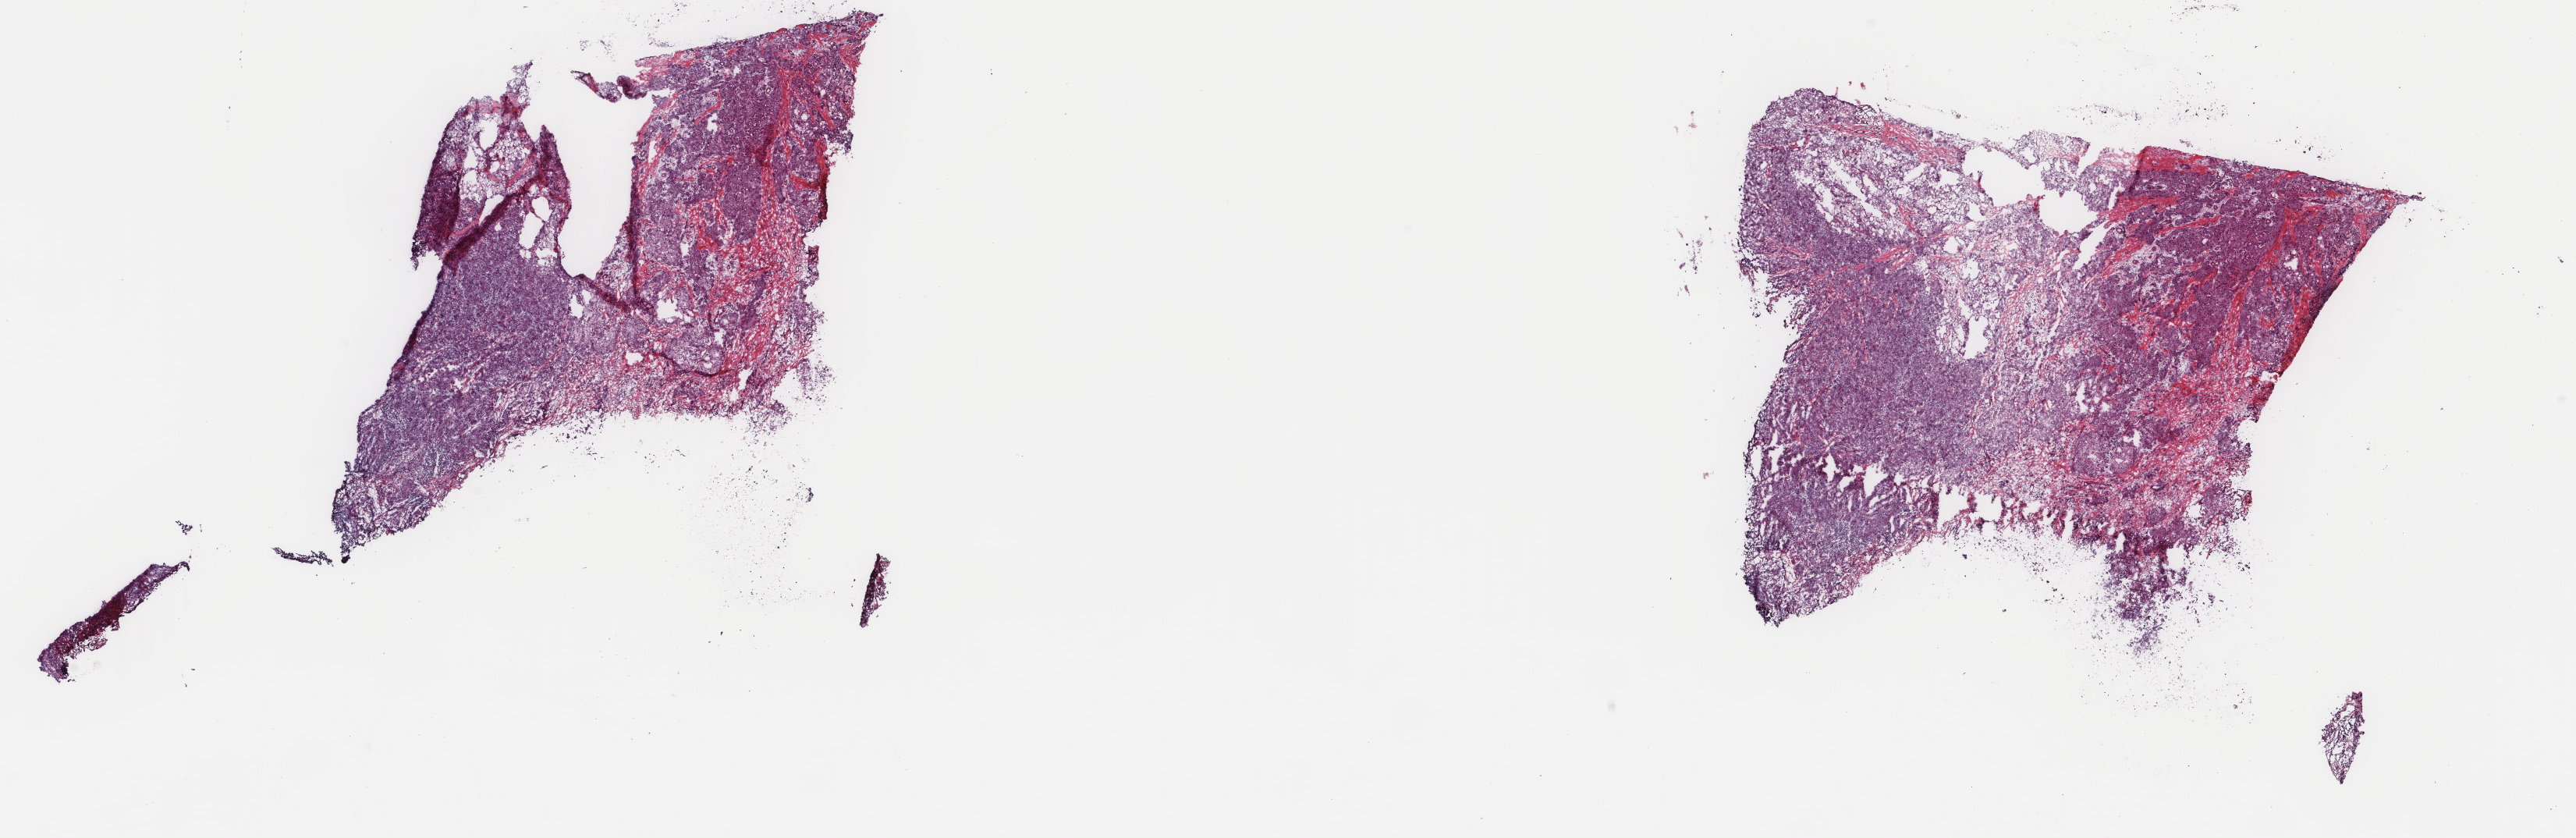
H&E-stained whole-slide image — a low-resolution overview of the entire scanned area, about 26.2 x 8.5 mm. Frozen section from the top of the tissue portion. Primary tumour sample from the liver. Female, age 75 years at initial diagnosis. Pathologist review of this section (percent, as recorded): tumour cells 100%, tumour nuclei 90%.
Diagnosis: Hepatocellular carcinoma, NOS.